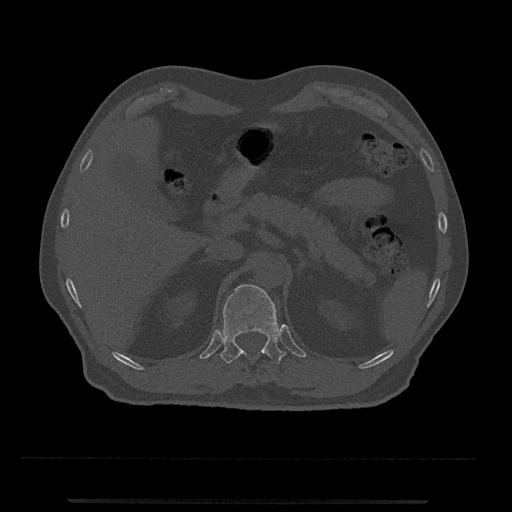
CT including the spine, one axial slice. Position 413 of 797 along the scan axis. 120 kVp. Bone window (W 1800 / L 400 HU). 512 × 512 image matrix. Patient: male, 63 years. Case-level facts recorded for this patient, not image findings: primary cancer: prostate.
Structures marked on this image (semi-automatic segmentation, software-assisted and operator-edited):
- T11 vertebra: bounding box (x1, y1, x2, y2) in pixels: (243, 352, 246, 354)
- T12 vertebra: (220, 284, 286, 364)